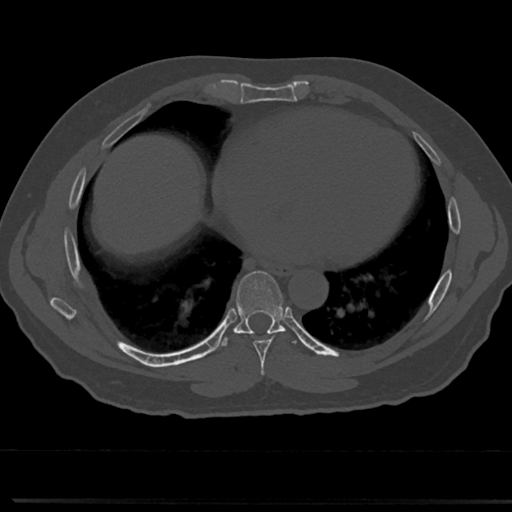
CT including the spine, one axial slice. Slice 375 of 817 in the series (ordered by position). 120 kVp. Bone window (W 1800 / L 400 HU). 0.5 mm slice thickness. 512 × 512 image matrix. Male patient, age 61 years. Case-level facts recorded for this patient, not image findings: primary cancer: prostate.
Structures marked on this image (semi-automatic segmentation, software-assisted and operator-edited):
- T7 vertebra: bounding box (x1, y1, x2, y2) in pixels: (234, 272, 289, 356)
- T8 vertebra: (238, 326, 281, 333)